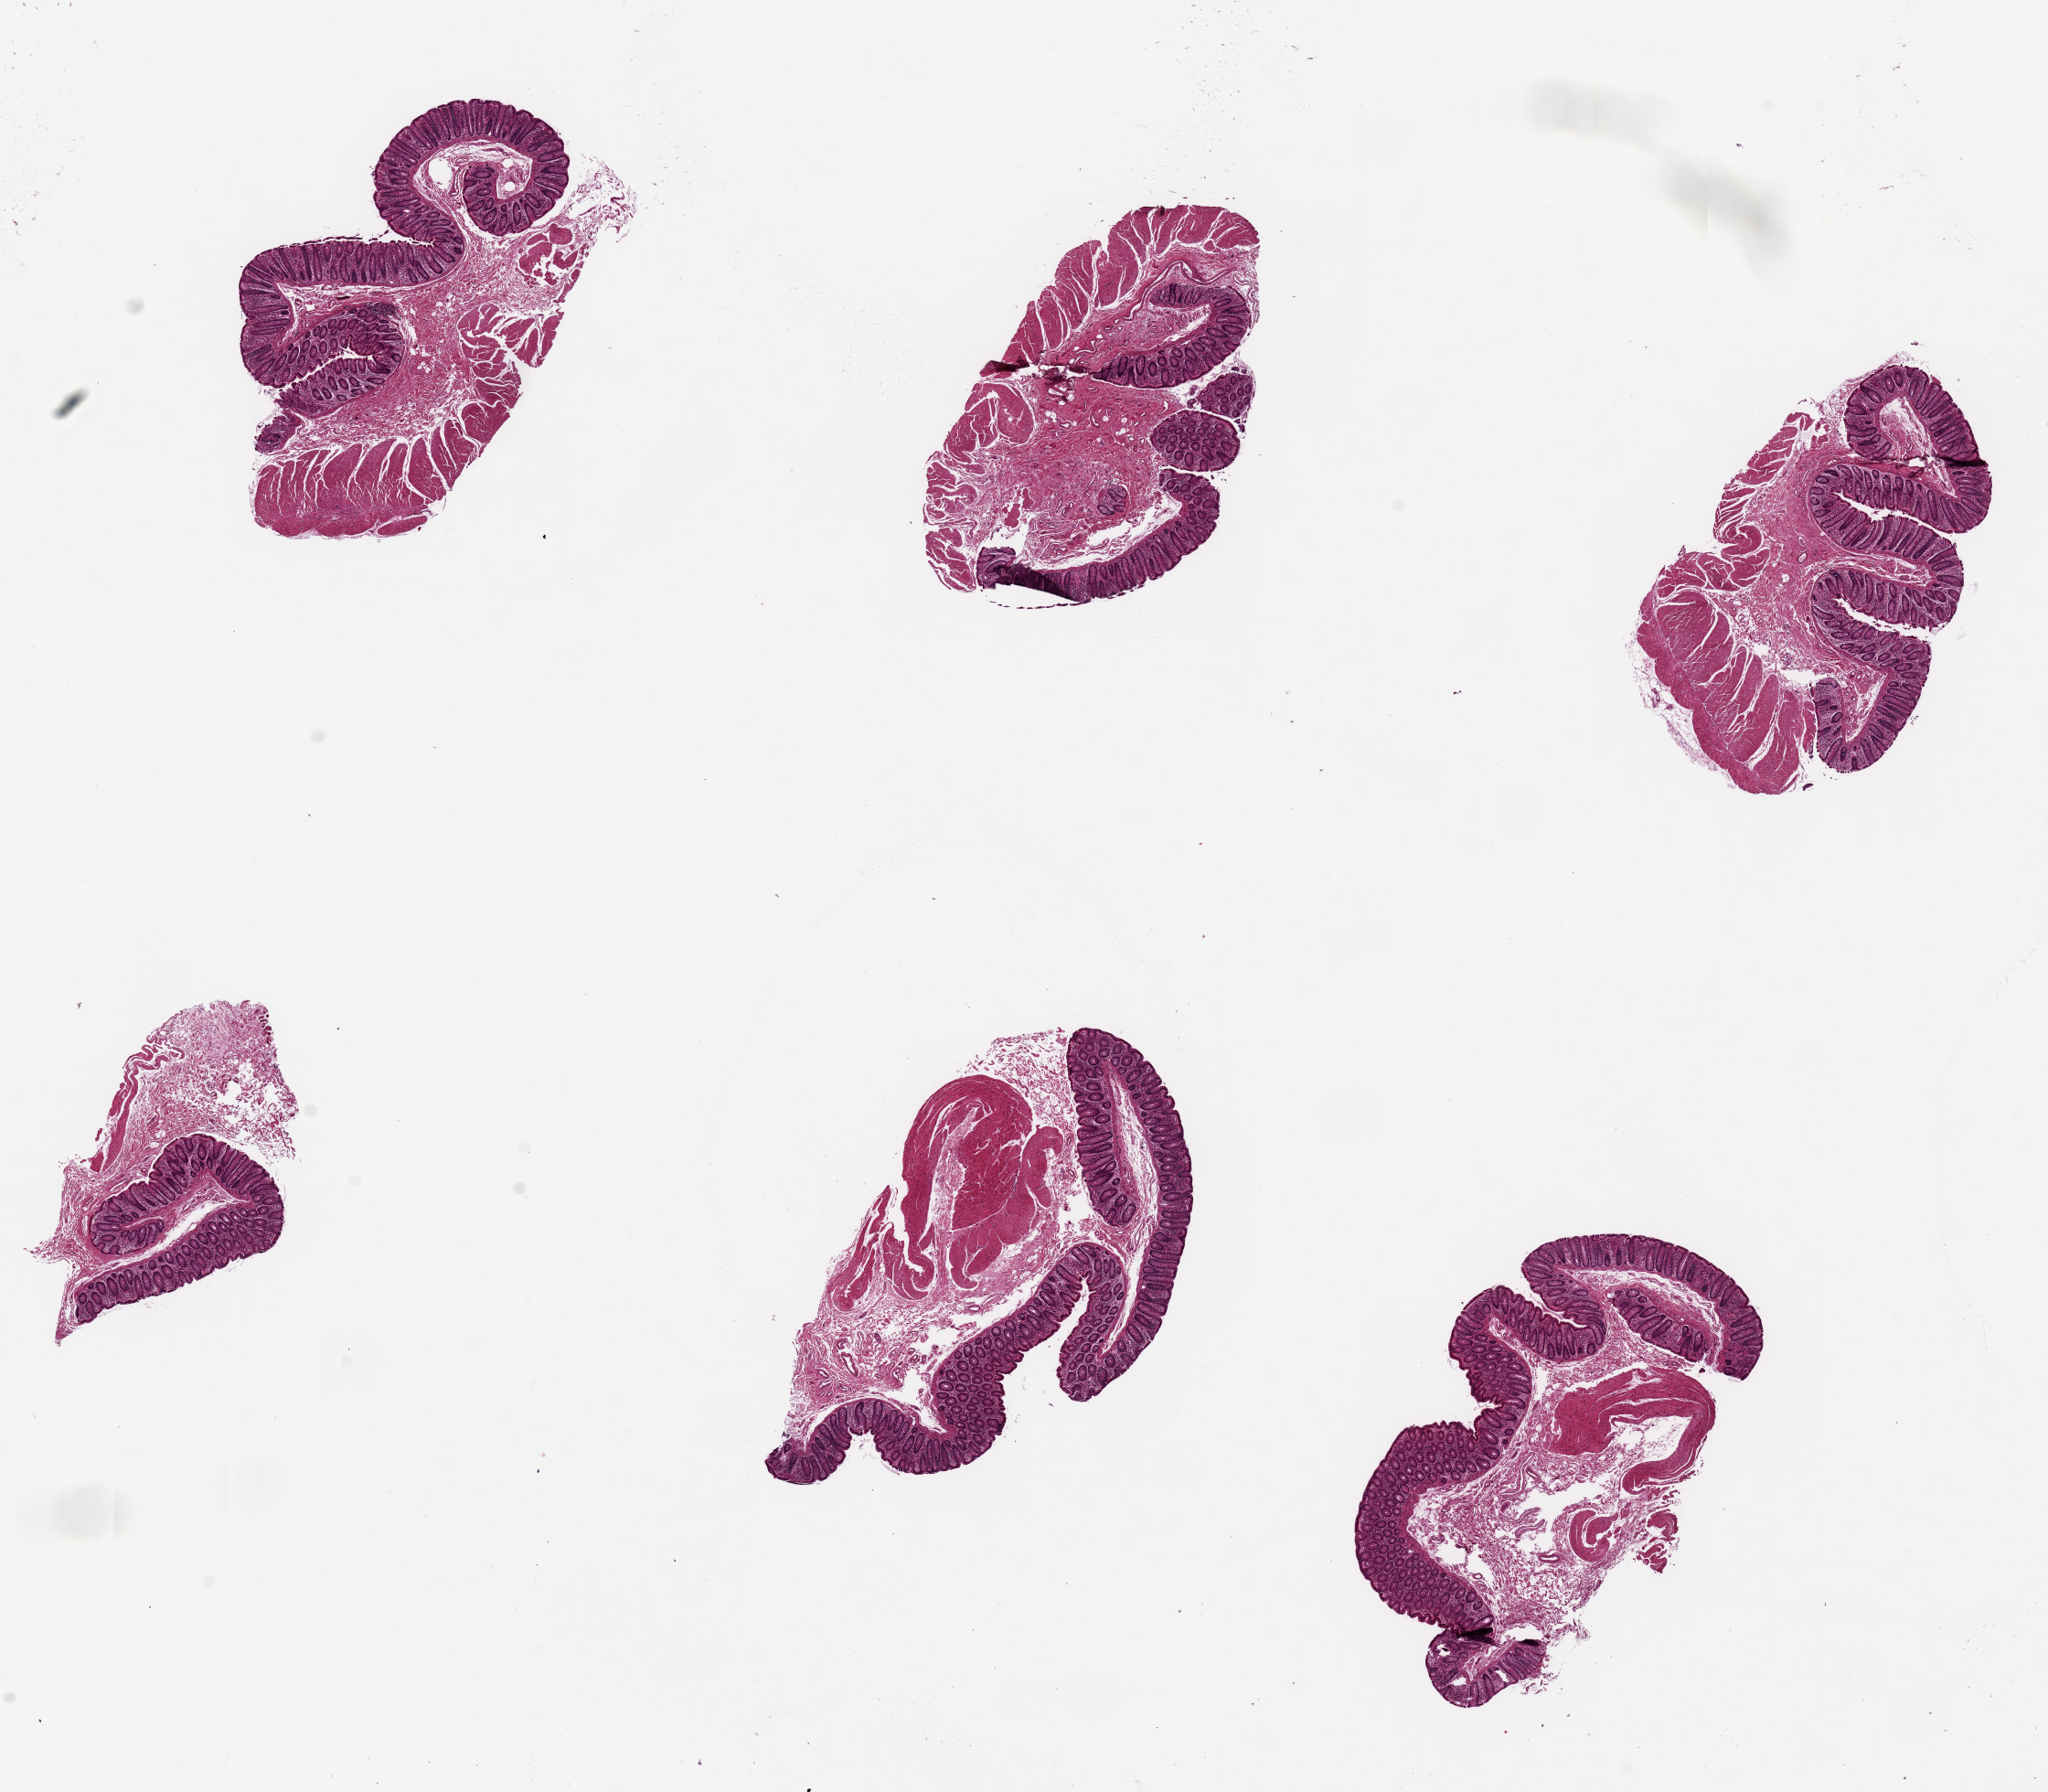
H&E whole-slide image, brightfield, whole scanned area (about 17.7 x 15.5 mm, slide scanned at 20x) shown as a low-resolution overview; PAXgene-fixed paraffin-embedded (PFPE) section; target tissue: transverse colon; donor tissue sample.
Review note (as recorded): 6 pieces, up to 5x3mm; ~10-20% thickness is fairly well-preserved mucosa.